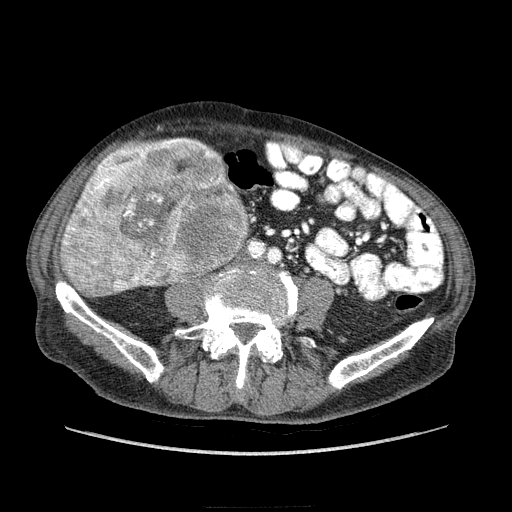
Contrast-enhanced abdominal CT (liver protocol), one axial slice. Slice 43 of 218 in the series (ordered by position). Reconstruction kernel STANDARD. Soft-tissue window (W 400 / L 40 HU). 2.5 mm slice thickness. 512 × 512 image matrix, field of view 380 × 380 mm. From the clinical record (not read from this slice): diagnosis: hepatocellular carcinoma (patient treated with transarterial chemoembolisation; whether this scan precedes or follows treatment is not stated here); TNM stage (as recorded): Stage-IIIA; Child-Pugh class: A; tumour differentiation: well differentiated; tumour nodularity: multinodular.
Structures marked on this image (semi-automatic segmentation, software-assisted and operator-edited):
- liver parenchyma outside the tumour (the mass and vessels are separate outlines, so this box may not span the whole liver): box from (x=60, y=160) to (x=248, y=296) px
- mass: (x=62, y=138)–(x=248, y=296)